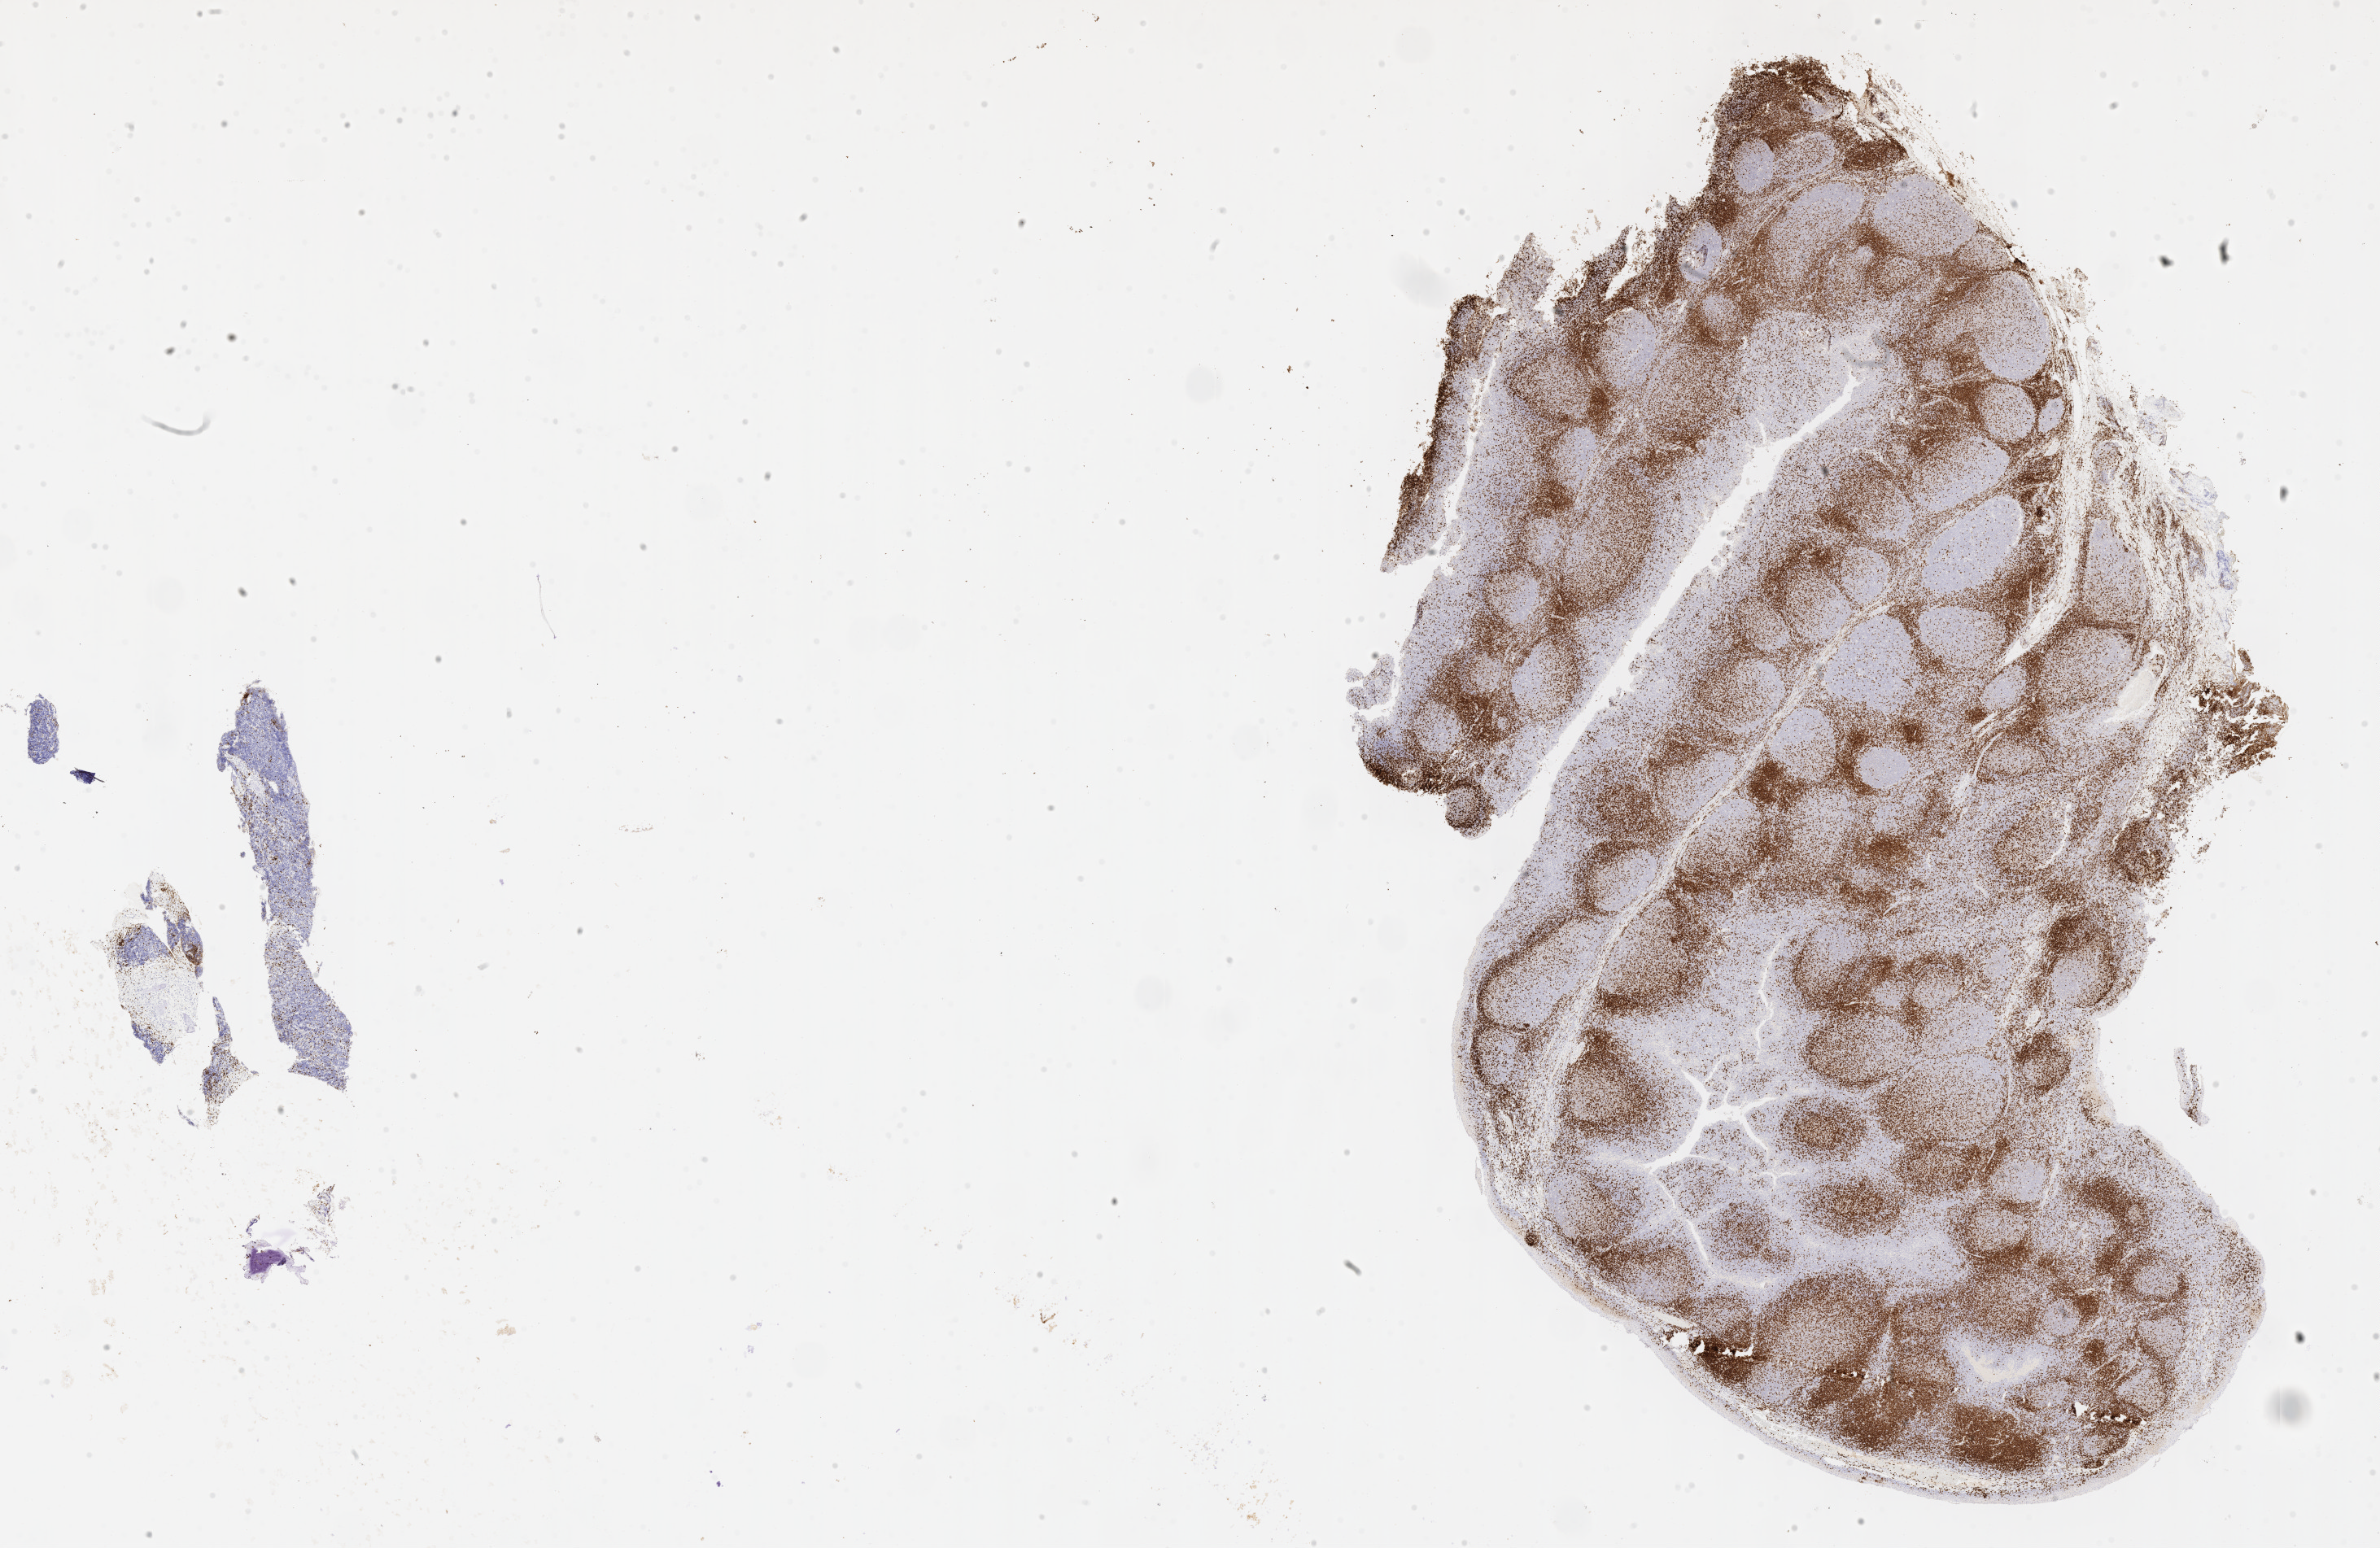
IHC for CD3, whole-slide image, shown as a low-resolution overview of the whole scanned area (about 23.6 x 15.4 mm), tumor tissue, anatomic site: mandible. Patient: male, age at initial diagnosis 6 years.
Histologic diagnosis: Burkitt lymphoma, NOS.